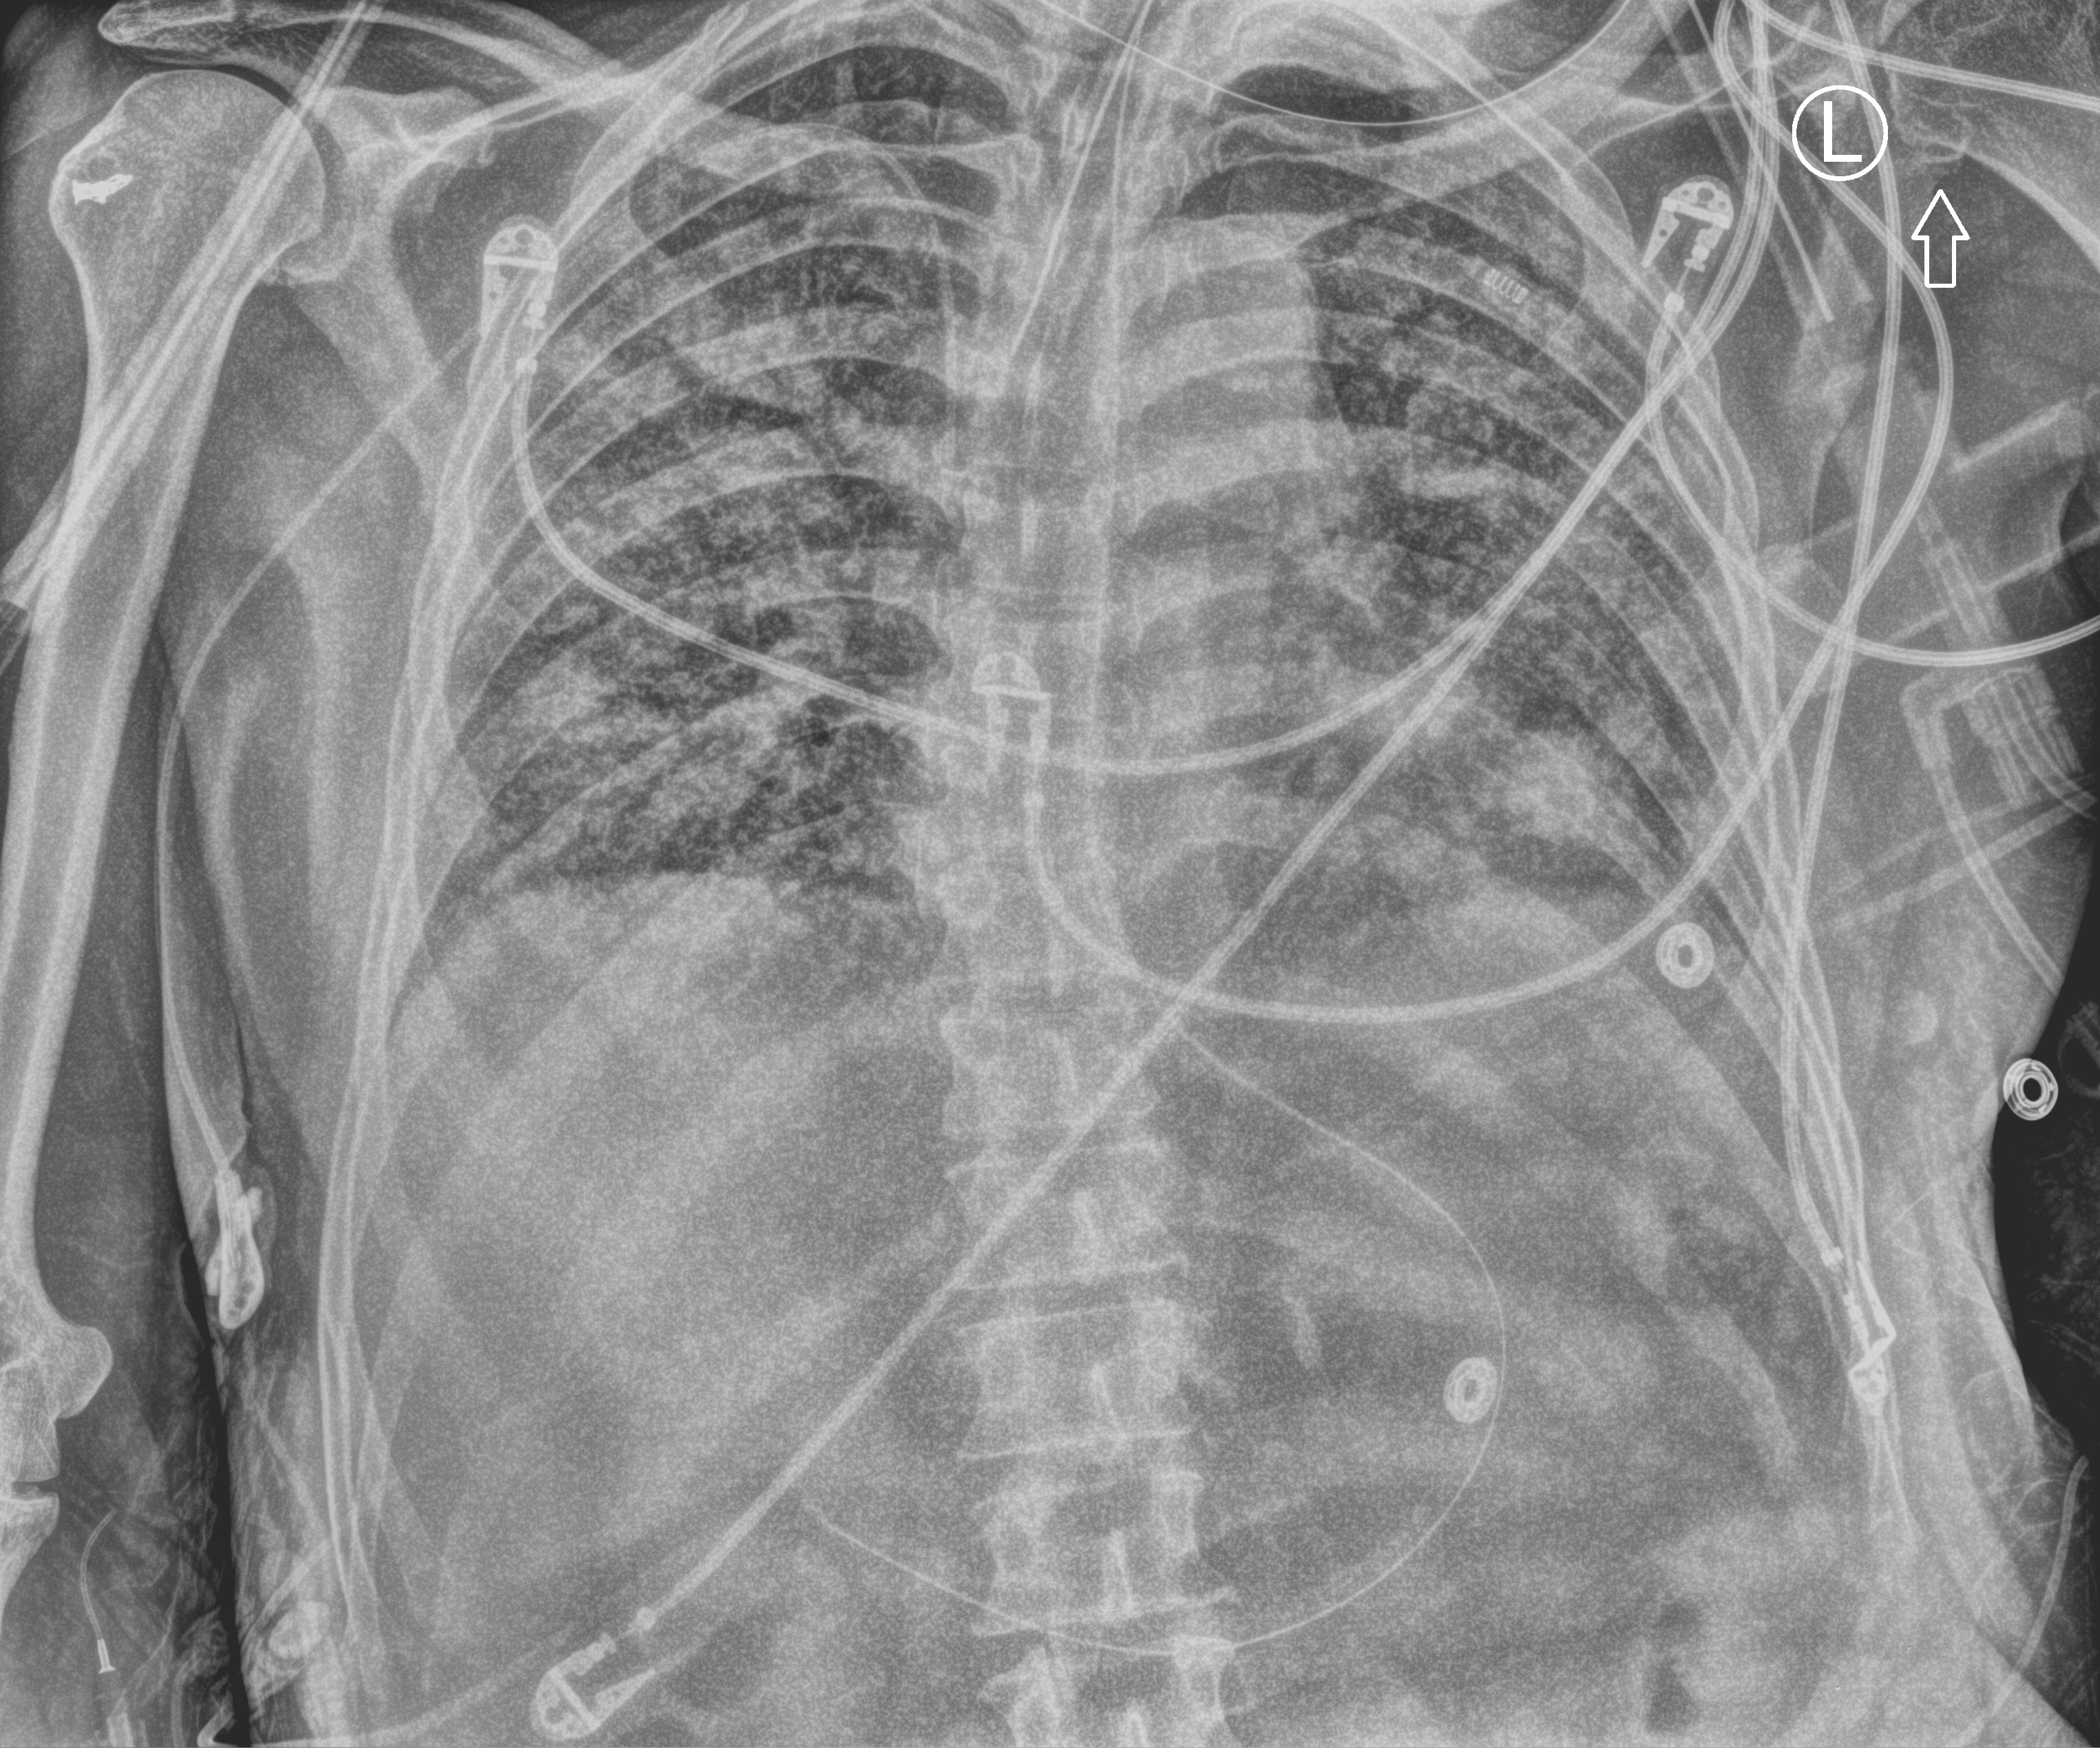
Chest X-ray (portable); anteroposterior (AP) projection. Male patient hospitalised with COVID-19, age 60–74 years.
From the hospital-stay record, not from the radiograph (when in the stay this image was taken is not recorded): mechanically ventilated during this hospital stay: yes; diabetes (admission record): no.